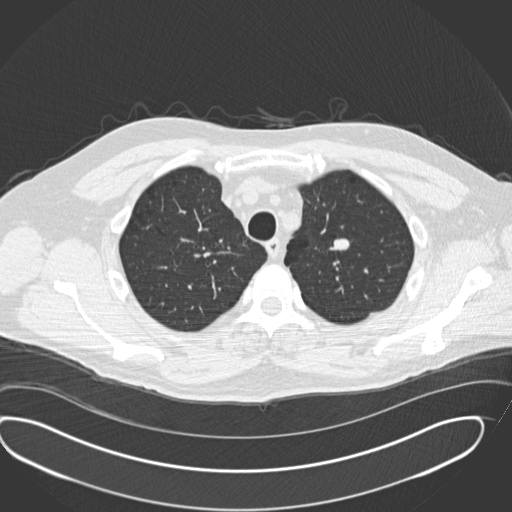
Chest CT (low-dose screening protocol), one axial image. Second annual screen. Lung window (W 1500 / L -600 HU). Standard (soft-tissue) reconstruction kernel (B30f). Slice 43 of 190 in the series. Male participant, aged 56 years at enrolment.
• Lesion marked by an expert reader, bounding box <312,226,368,270> (left, top, right, bottom; pixels).
• No non-calcified nodule or mass ≥4 mm was recorded by the screening reader at this exam.
• Participant outcome: lung cancer diagnosed 520 days after this screen (after the third annual screen) — neuroendocrine carcinoma, NOS, left upper lobe, well differentiated (G1), stage IA (AJCC 6th edition), 20 mm at pathology.